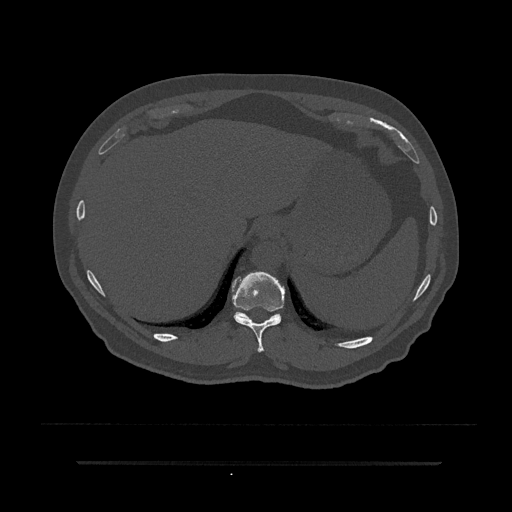
CT including the spine, one axial slice. Slice 311 of 797 in the series (ordered by position). Reconstruction kernel Br40s/3. 120 kVp. Bone window (W 1800 / L 400 HU). 0.5 mm slice thickness. 512 × 512 image matrix, field of view 464 × 464 mm. Male patient, age 59 years. From the clinical record (not read from this slice): primary cancer: bile ducts.
Annotated regions visible in this slice (semi-automatically segmented with operator editing):
- T10 vertebra: box from (x=232, y=272) to (x=285, y=352) px
- T11 vertebra: (x=235, y=272)–(x=281, y=321)